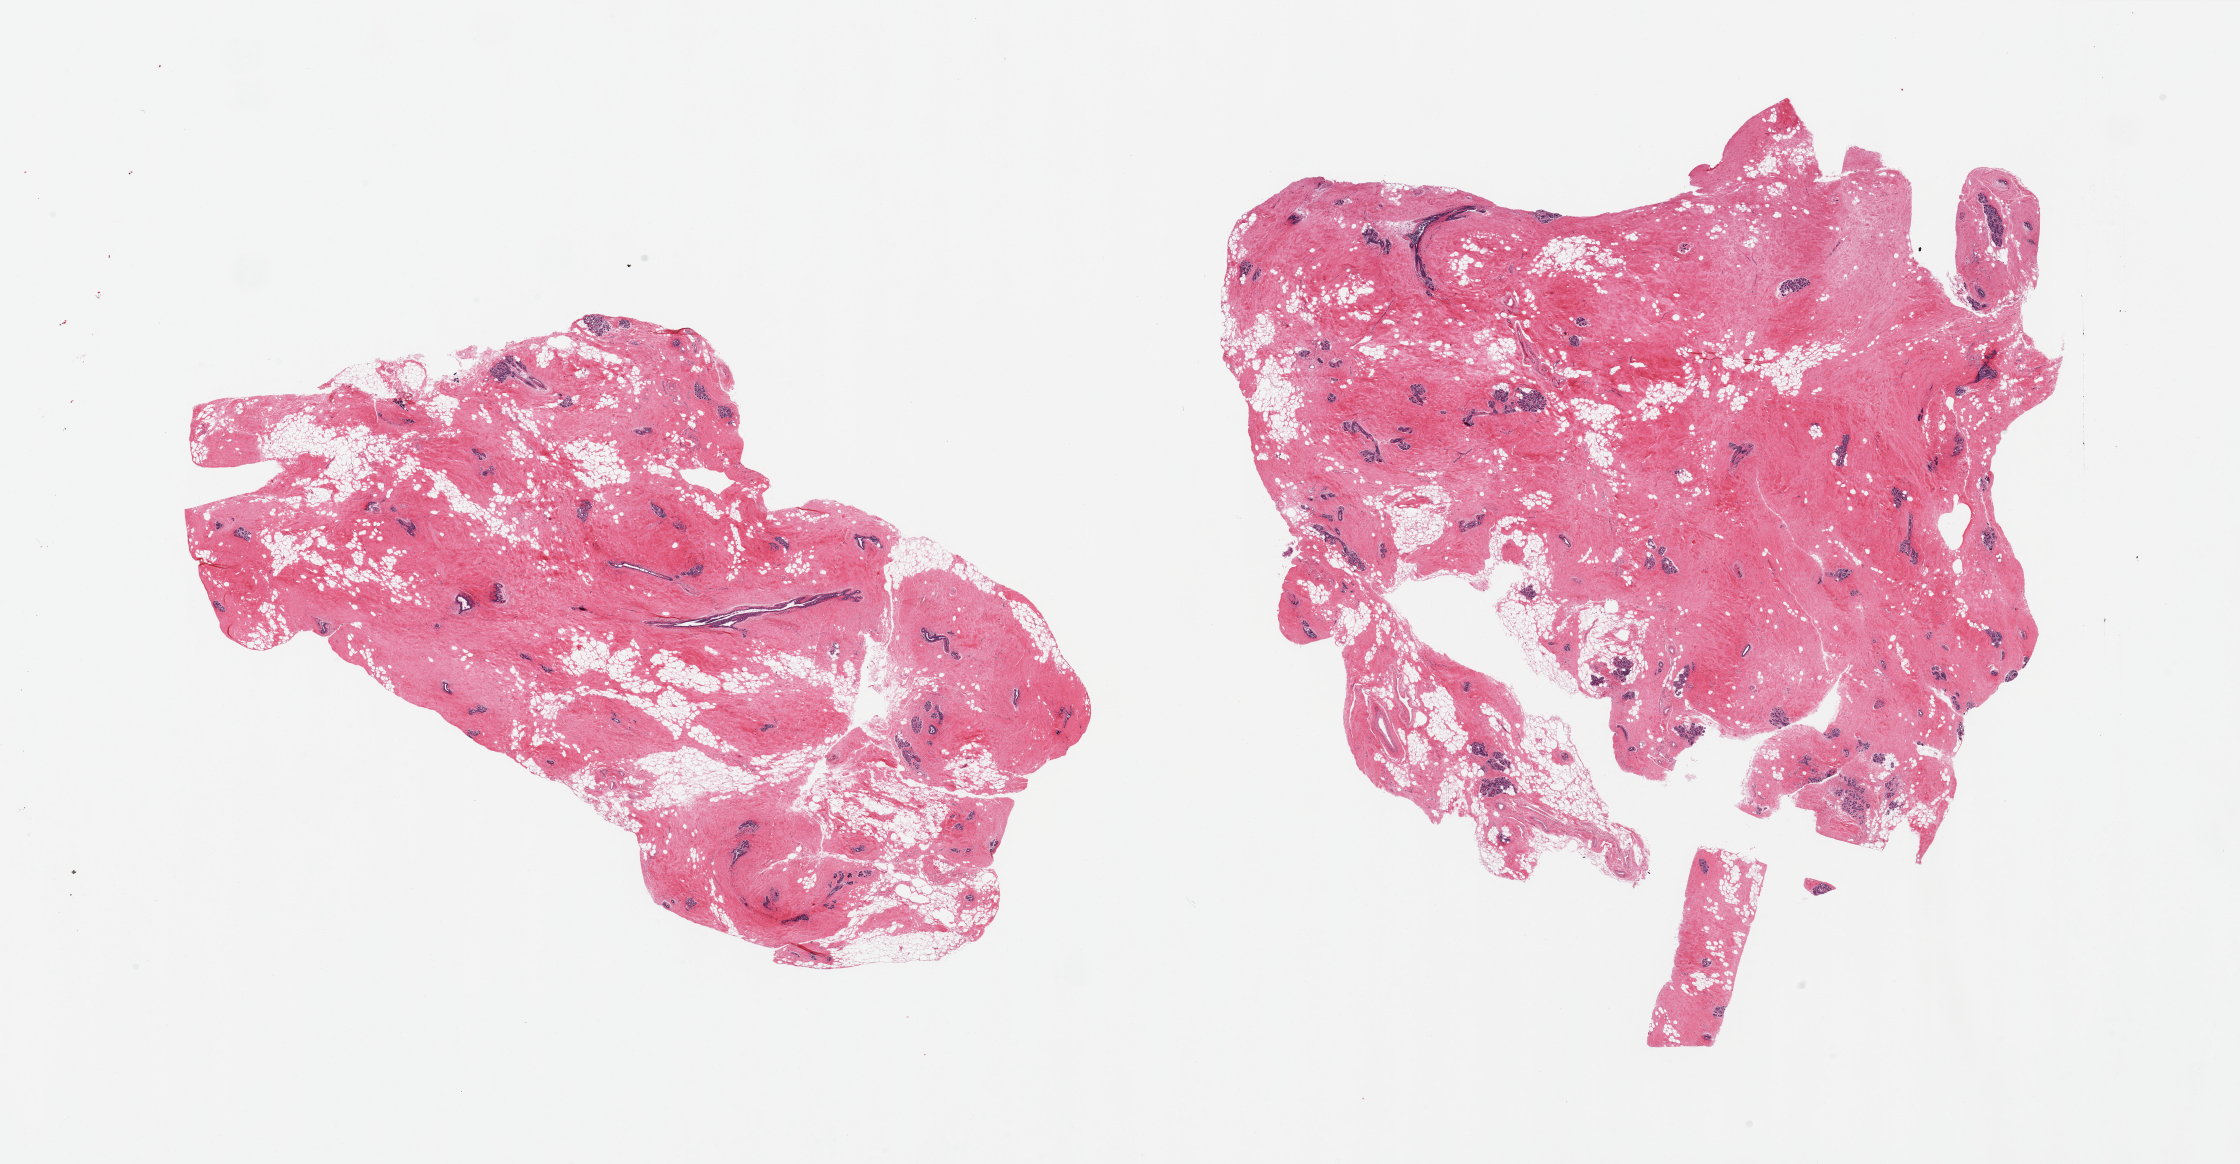
H&E whole-slide image — whole scanned area (about 35.4 x 18.4 mm, from a 20x scan) shown as a low-resolution overview, PAXgene-fixed, paraffin-embedded tissue, sampled site (target tissue): breast, tissue donor sample.
- review note (as recorded): 2 pieces; fat and fibrocollagenous stroma with embedded ductal and lobular structures